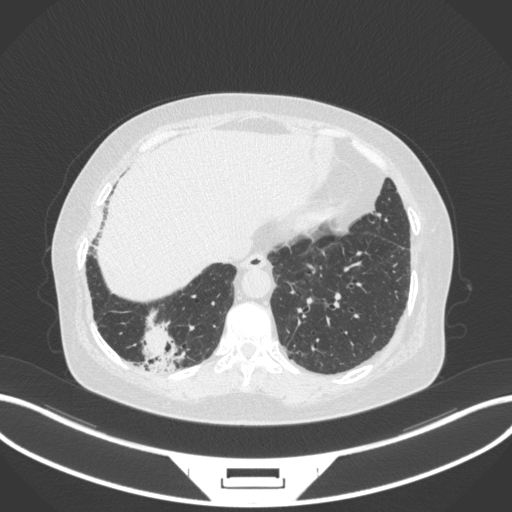
Chest CT, one axial slice; slice 34 of 303 in the series (ordered by position); reconstruction kernel B31f; 120 kVp; lung window (W 1500 / L -600 HU); 1 mm slice thickness; 512 × 512 image matrix, field of view 400 × 400 mm. Female patient, age 65 years. Case-level facts recorded for this patient, not image findings: clinical TNM (as recorded): T2b N1 M0; histopathological grade: G1.
Structures marked on this image (bounding box drawn by a radiologist):
- lung tumour (recorded histology: adenocarcinoma): bounding box (x1, y1, x2, y2) in pixels: (135, 308, 190, 374)